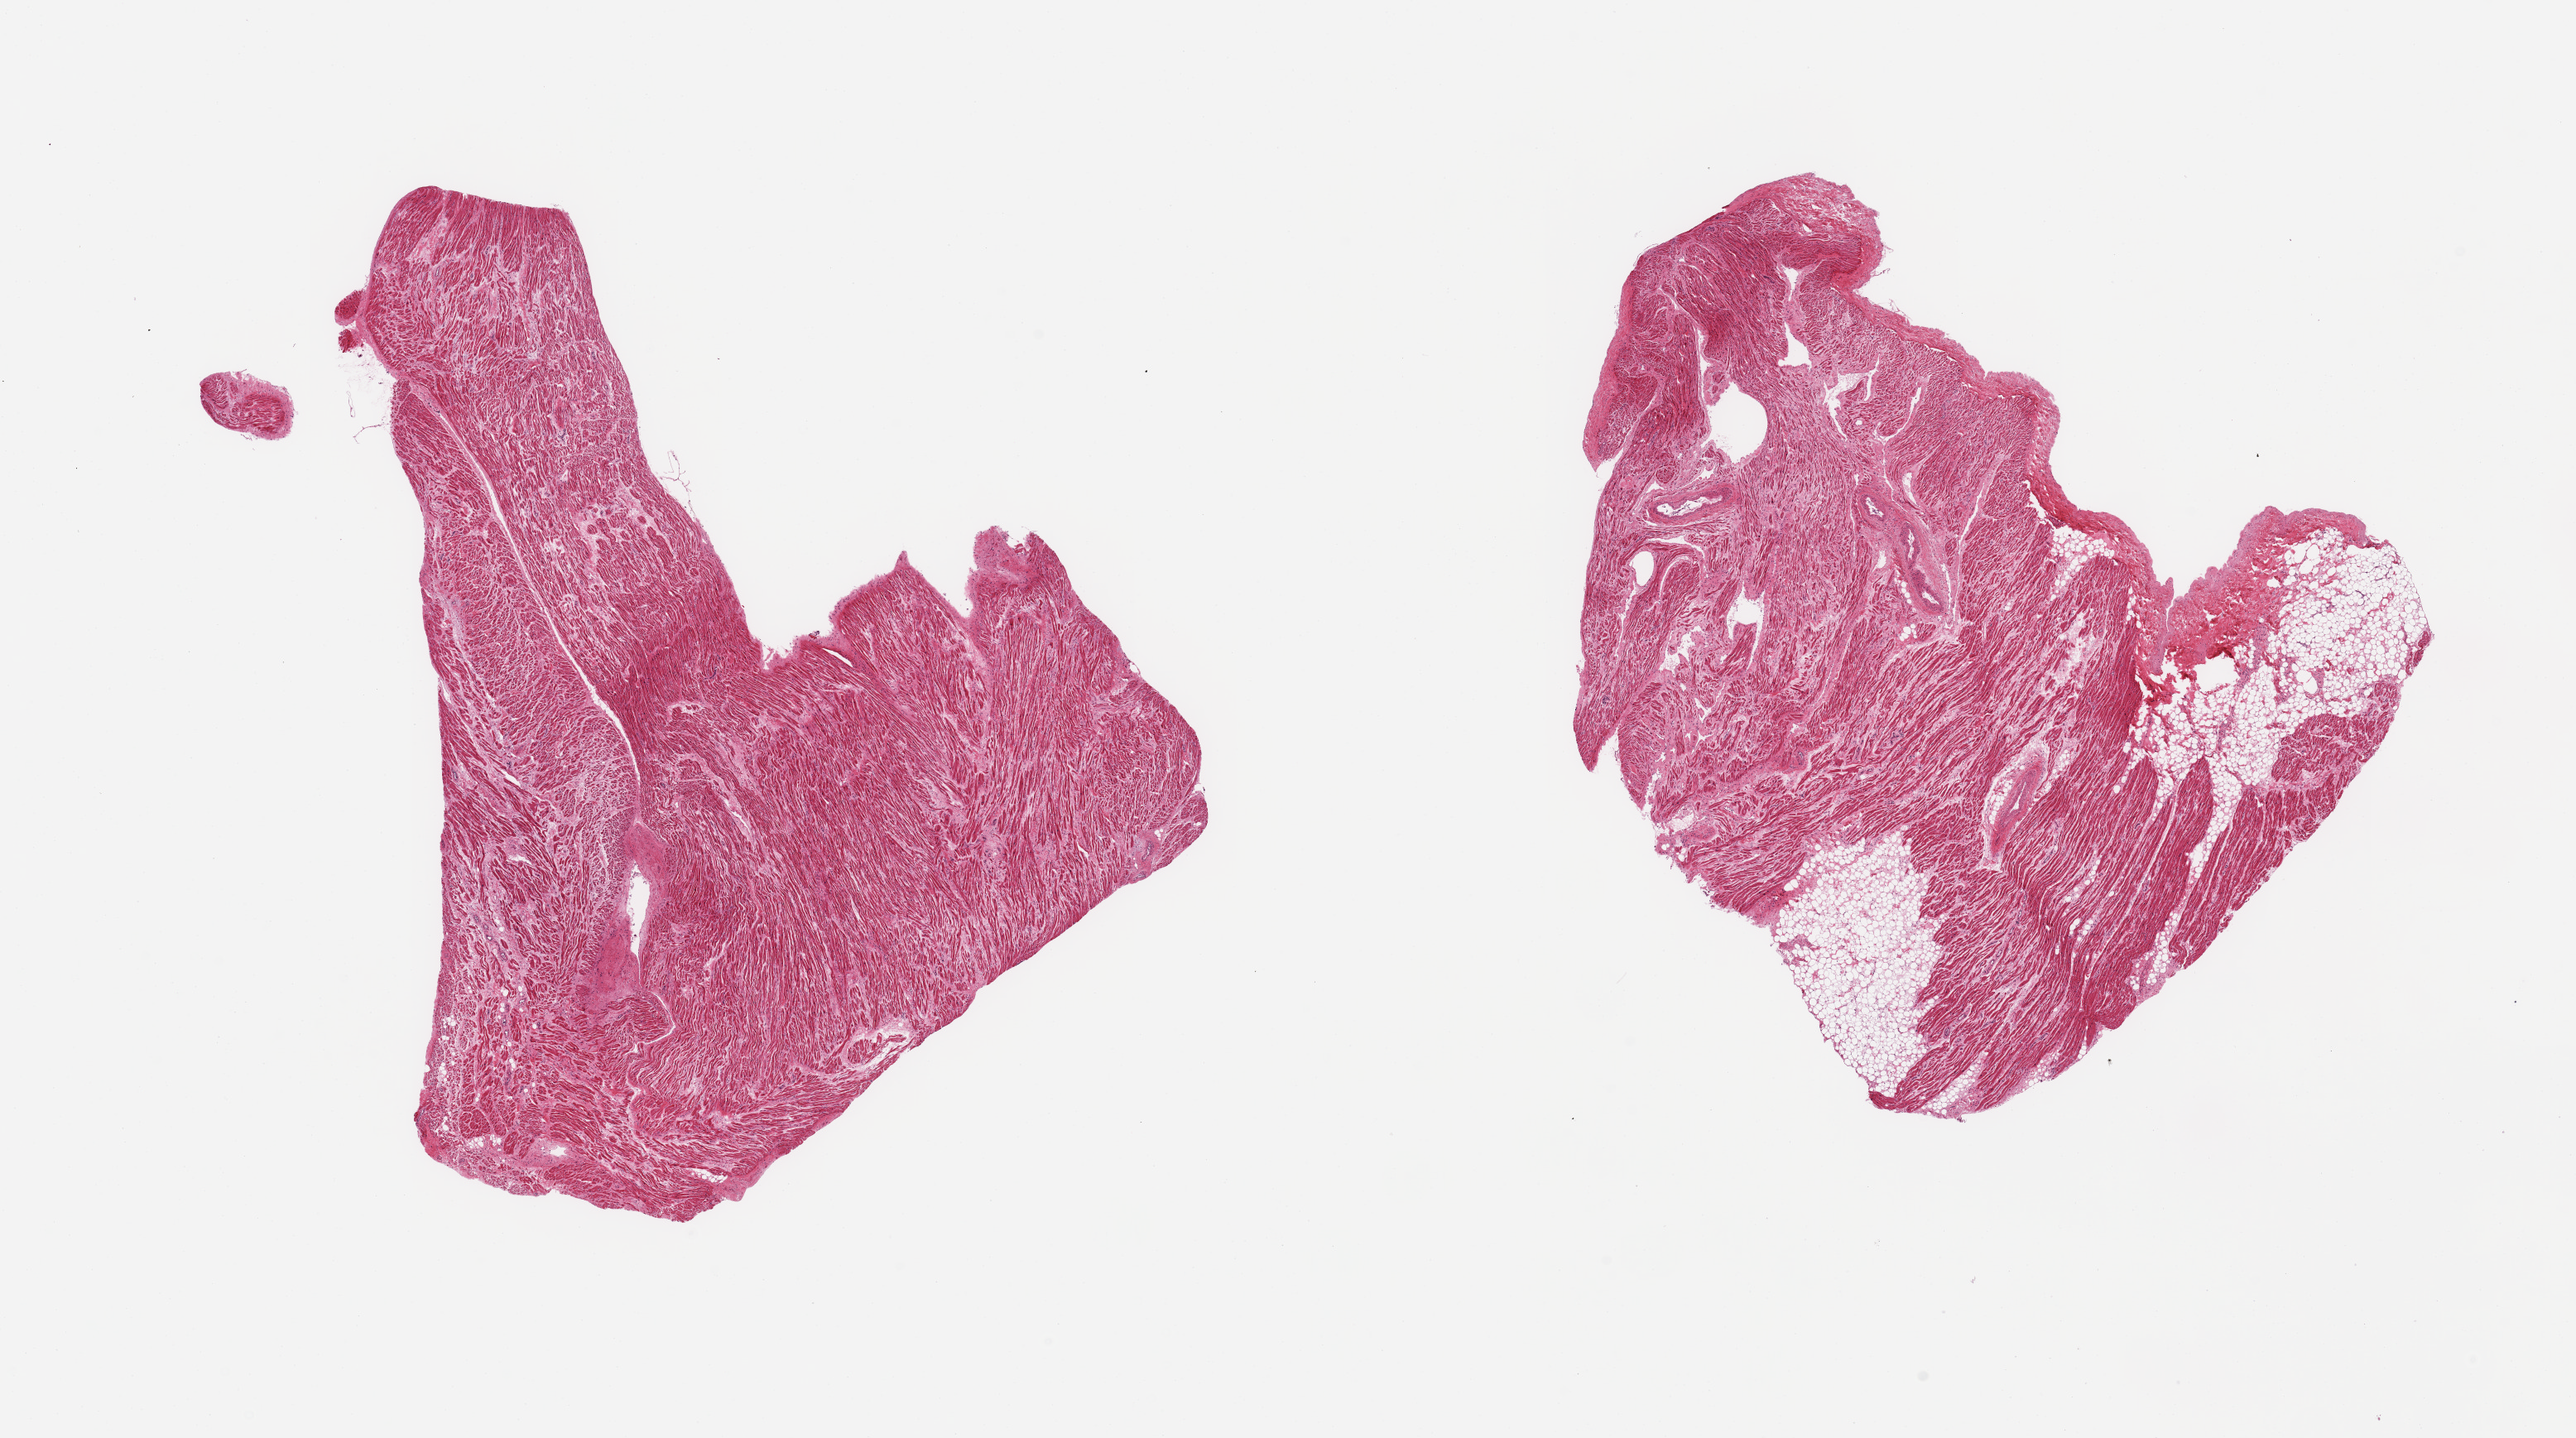
Digitized H&E-stained section — a low-resolution overview of the entire scanned area, about 24.6 x 13.7 mm (slide scanned at 20x), PAXgene-fixed paraffin-embedded (PFPE) section, sampled site (target tissue): auricular appendage, tissue donor sample. Donor sex: male.
Pathologist's review note for this sample: 2 pieces, no abnormalities.